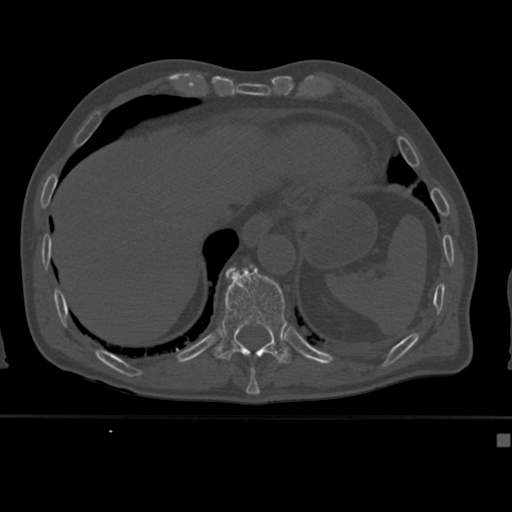
CT including the spine, one axial slice; slice 214 of 430 in the series (ordered by position); reconstruction kernel Br40s; 120 kVp; bone window (W 1800 / L 400 HU); 1.5 mm slice thickness; 512 × 512 image matrix, field of view 337 × 337 mm. Patient: male, 64 years. From the clinical record (not read from this slice): primary cancer: uterus.
Annotated regions visible in this slice (semi-automatic segmentation, software-assisted and operator-edited):
- T10 vertebra: bounding box [x1, y1, x2, y2] px = [250, 366, 256, 382]
- T11 vertebra: [214, 265, 291, 364]
- T12 vertebra: [231, 266, 237, 270]